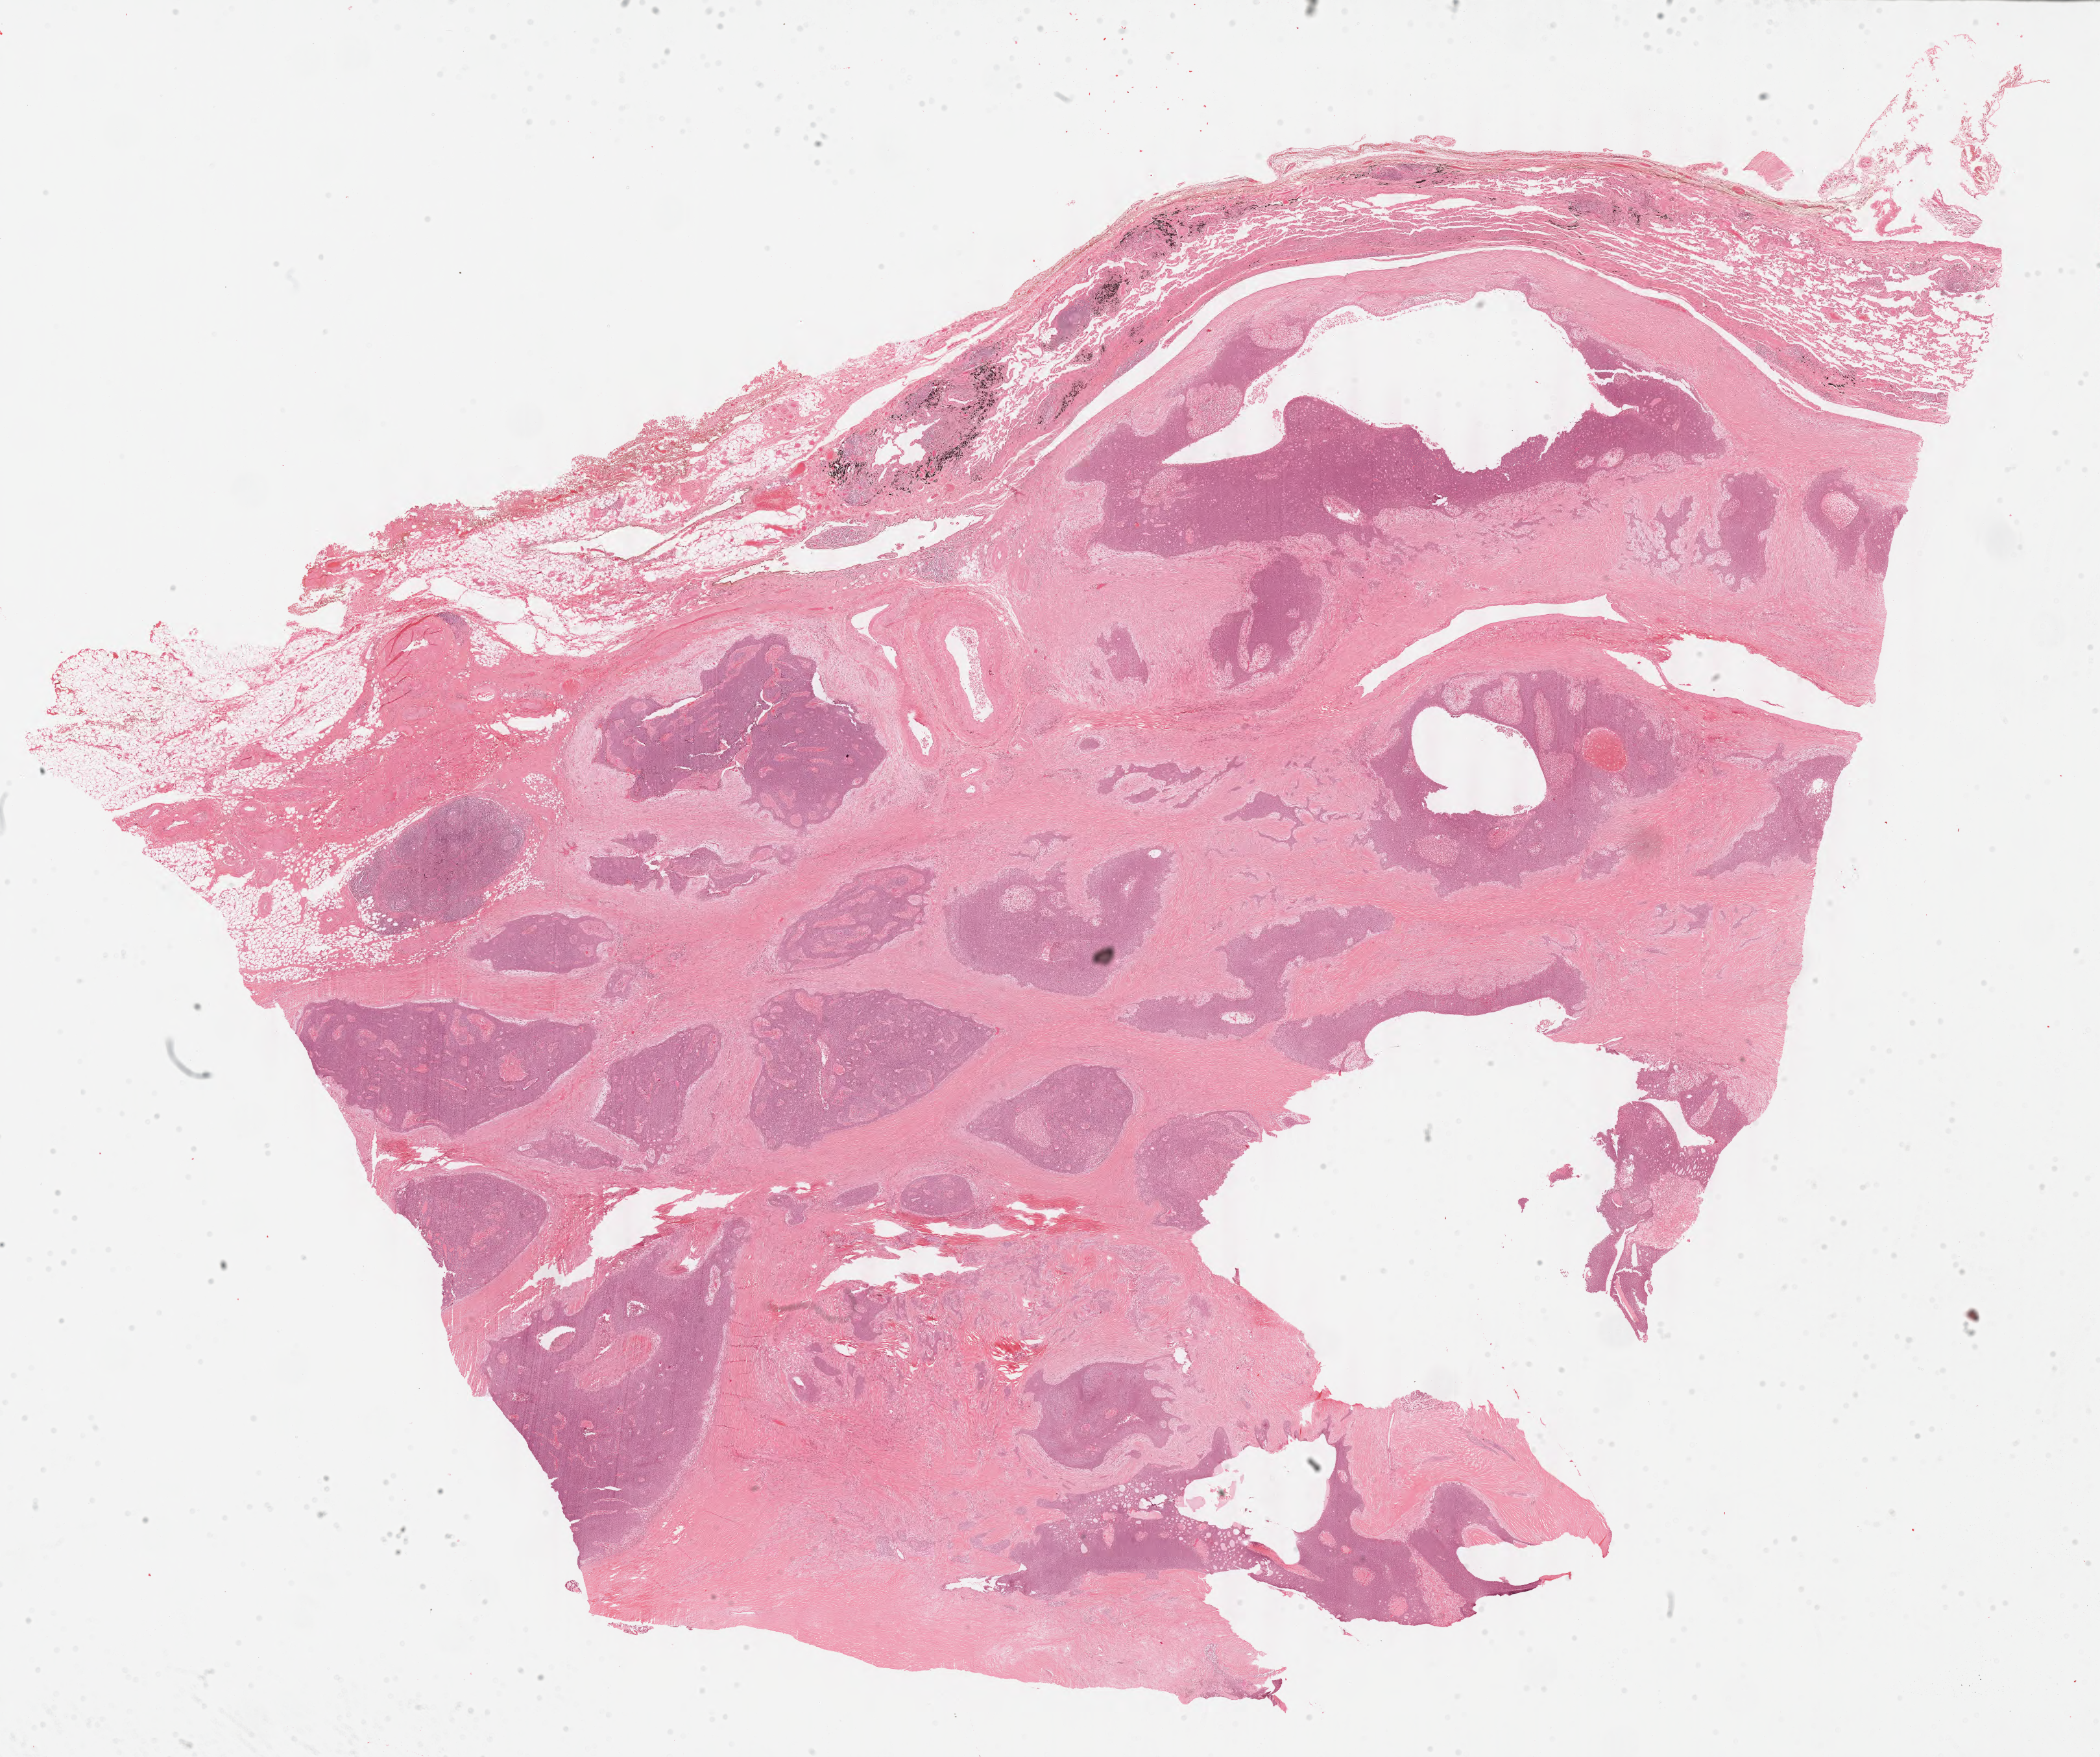
Digitized H&E-stained tissue section (whole slide) — shown as a low-resolution overview of the whole scanned area (about 25.6 x 21.4 mm). Formalin-fixed paraffin-embedded (FFPE) diagnostic section. Thymus, primary tumour sample. Patient: male, age at initial diagnosis 76 years.
Diagnosis: Thymic carcinoma, NOS.